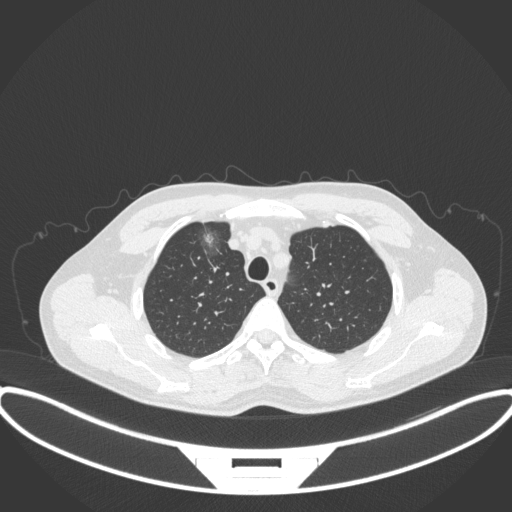
Chest CT, one axial slice. Slice 295 of 395 in the series (ordered by position). 120 kVp. Lung window (W 1500 / L -600 HU). 512 × 512 image matrix, field of view 424 × 424 mm. Male patient, age 60 years. From the clinical record (not read from this slice): clinical TNM (as recorded): T1c N0 M0.
Outlined on this slice (rectangle marked by the reading radiologist):
- lung tumour (recorded histology: adenocarcinoma): box from (x=194, y=224) to (x=223, y=260) px